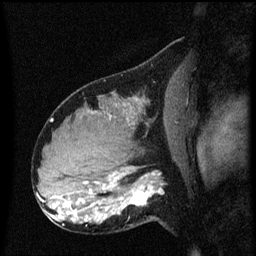
Breast MRI (dynamic contrast-enhanced), one sagittal slice; position 34 of 60 along the scan axis; dynamic contrast-enhanced series, image 2 of 3 at this slice position (ordered by acquisition); 1.5 T; TE 4.2 ms, TR 8.4 ms; 2 mm slice thickness; 256 × 256 image matrix, field of view 200 × 200 mm. Patient: female, 31 years. Case-level facts recorded for this patient, not image findings: setting: breast cancer imaged before/during neoadjuvant chemotherapy; receptor status: HR-positive, HER2-negative.
Annotated regions visible in this slice (semi-automatically segmented with operator editing):
- analysis volume of interest (the breast-tissue region the enhancement analysis was run in; not a lesion): box from (x=102, y=166) to (x=168, y=229) px
- tumour enhancement mask (voxels above the 70 % enhancement threshold inside the analysis volume of interest): (x=102, y=174)–(x=163, y=221)